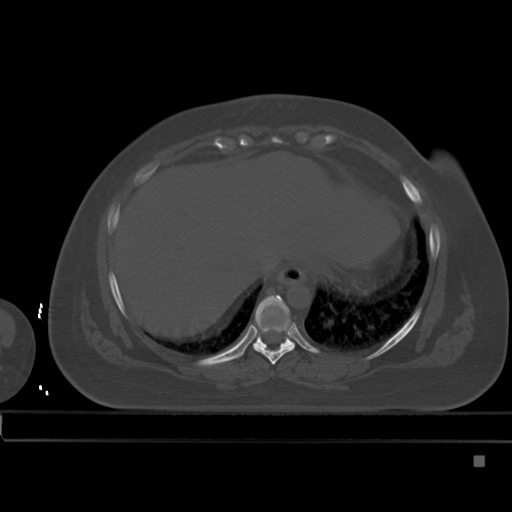
CT including the spine, one axial slice; slice 271 of 495 in the series (ordered by position); bone window (W 1800 / L 400 HU); 1.5 mm slice thickness; 512 × 512 image matrix, field of view 404 × 404 mm. Patient: female, 33 years. From the clinical record (not read from this slice): primary cancer: breast; vertebrae with lytic lesions (as recorded): T1.
Annotated regions visible in this slice (semi-automatic segmentation, software-assisted and operator-edited):
- T8 vertebra: bounding box [x1, y1, x2, y2] px = [253, 327, 295, 365]
- T9 vertebra: [253, 295, 295, 349]